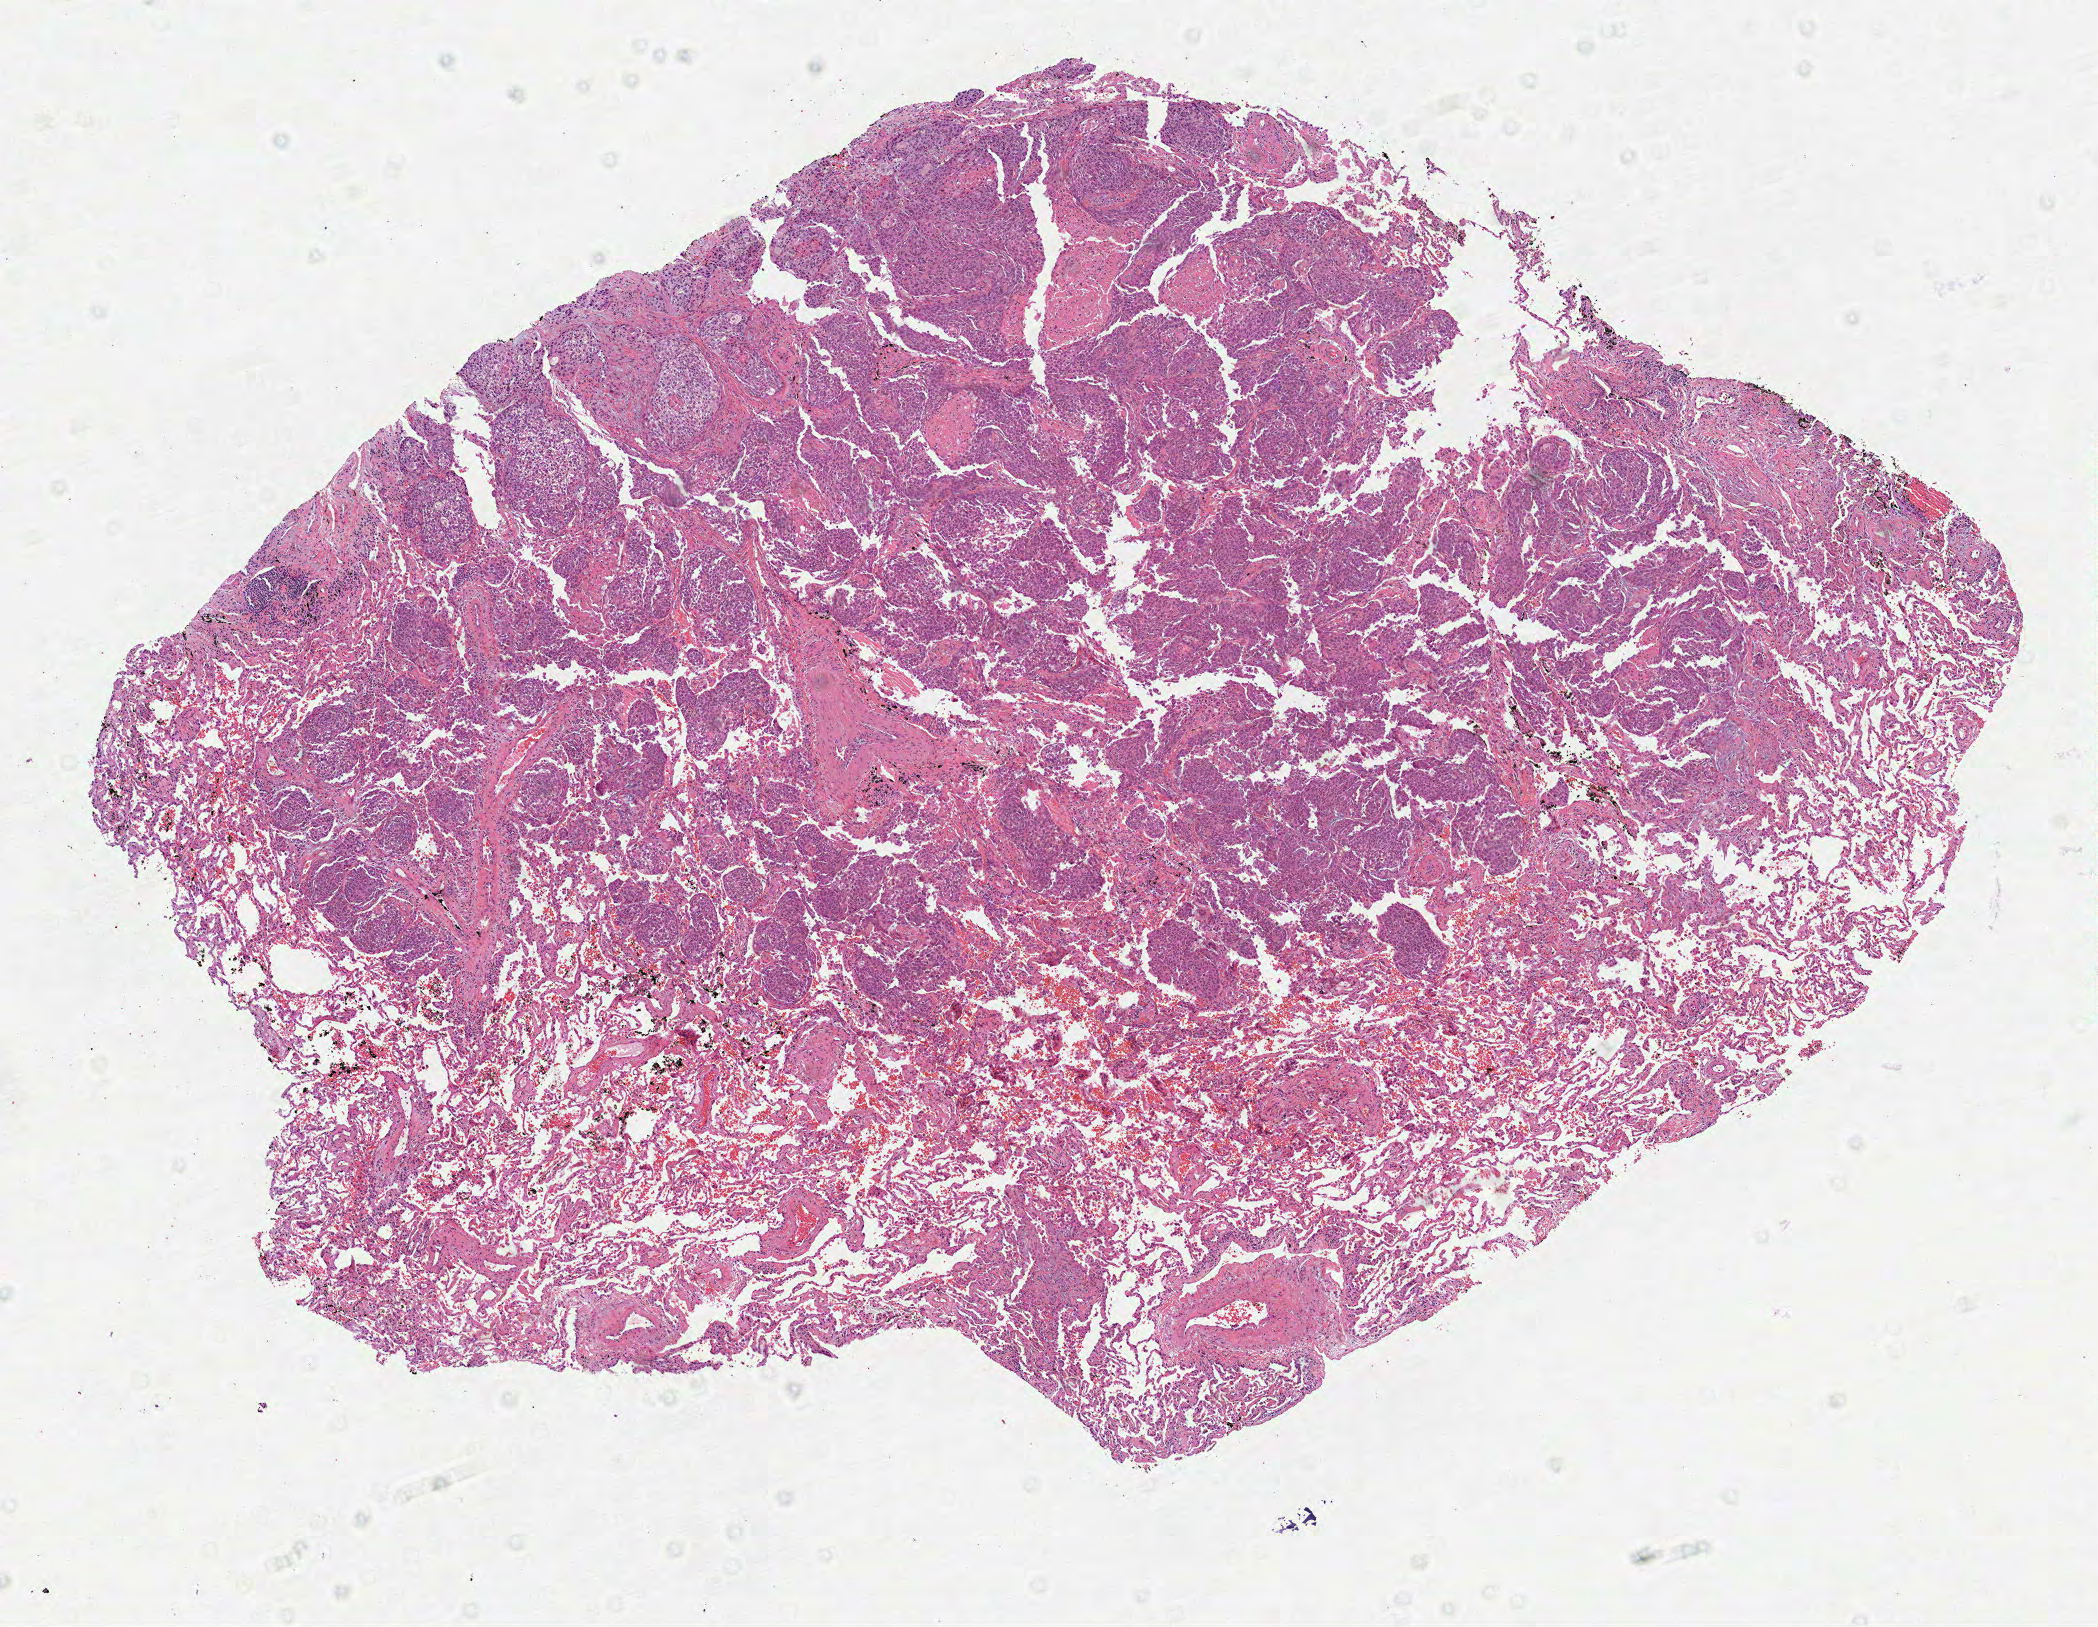
Hematoxylin and eosin (H&E) stained whole-slide image, shown as a low-resolution overview of the whole scanned area (about 8.5 x 6.6 mm, slide scanned at 40x). Formalin-fixed paraffin-embedded (FFPE) diagnostic section. Sample: primary tumour, lung. Male patient; age at initial diagnosis 79 years.
Diagnosis: Squamous cell carcinoma, NOS (lower lobe, lung). AJCC pathologic stage: IB (7th edition).